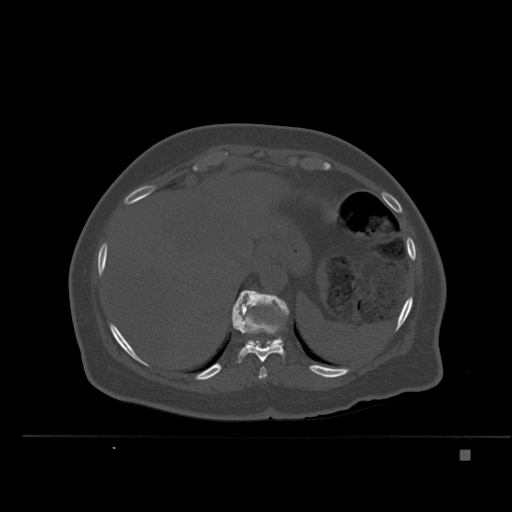
CT including the spine, one axial slice. Position 281 of 477 along the scan axis. Bone window (W 1800 / L 400 HU). 1.5 mm slice thickness. 512 × 512 image matrix, field of view 422 × 422 mm. Female patient, age 74 years. Case-level facts recorded for this patient, not image findings: primary cancer: colon.
Annotated regions visible in this slice (semi-automatic segmentation, software-assisted and operator-edited):
- T10 vertebra: bounding box <233,302,285,363> (left, top, right, bottom; pixels)
- T11 vertebra: <232,290,290,345>
- T9 vertebra: <258,367,267,379>